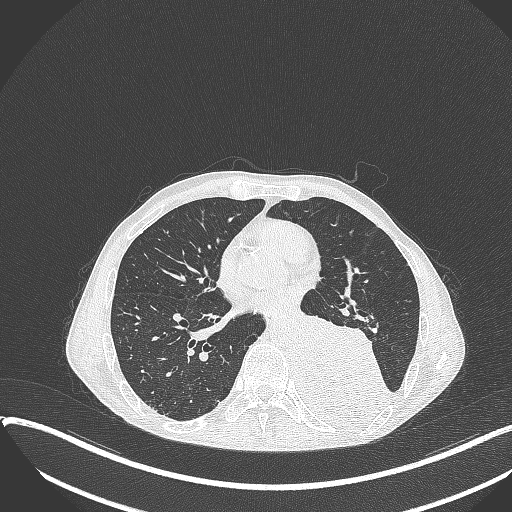
Chest CT, one axial slice. Position 160 of 401 along the scan axis. Lung window (W 1500 / L -600 HU). 512 × 512 image matrix, field of view 400 × 400 mm. Patient: male, 57 years. Case-level facts recorded for this patient, not image findings: clinical TNM (as recorded): T4 N0 M0.
Annotated regions visible in this slice (rectangle marked by the reading radiologist):
- lung tumour (recorded histology: squamous cell carcinoma): bounding box [x1, y1, x2, y2] px = [296, 307, 390, 438]